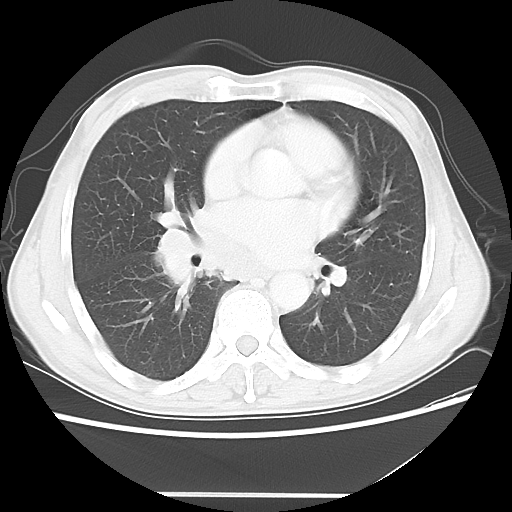
Chest CT, one axial slice. Position 26 of 56 along the scan axis. Reconstruction kernel LUNG. Lung window (W 1500 / L -600 HU). 5 mm slice thickness. 512 × 512 image matrix, field of view 344 × 344 mm. Patient: male, 65 years. Case-level facts recorded for this patient, not image findings: clinical TNM (as recorded): T1c N3 M0; histopathological grade: G3.
Annotated regions visible in this slice (rectangle marked by the reading radiologist):
- lung tumour (recorded histology: small cell carcinoma): bounding box [x1, y1, x2, y2] px = [154, 209, 230, 290]